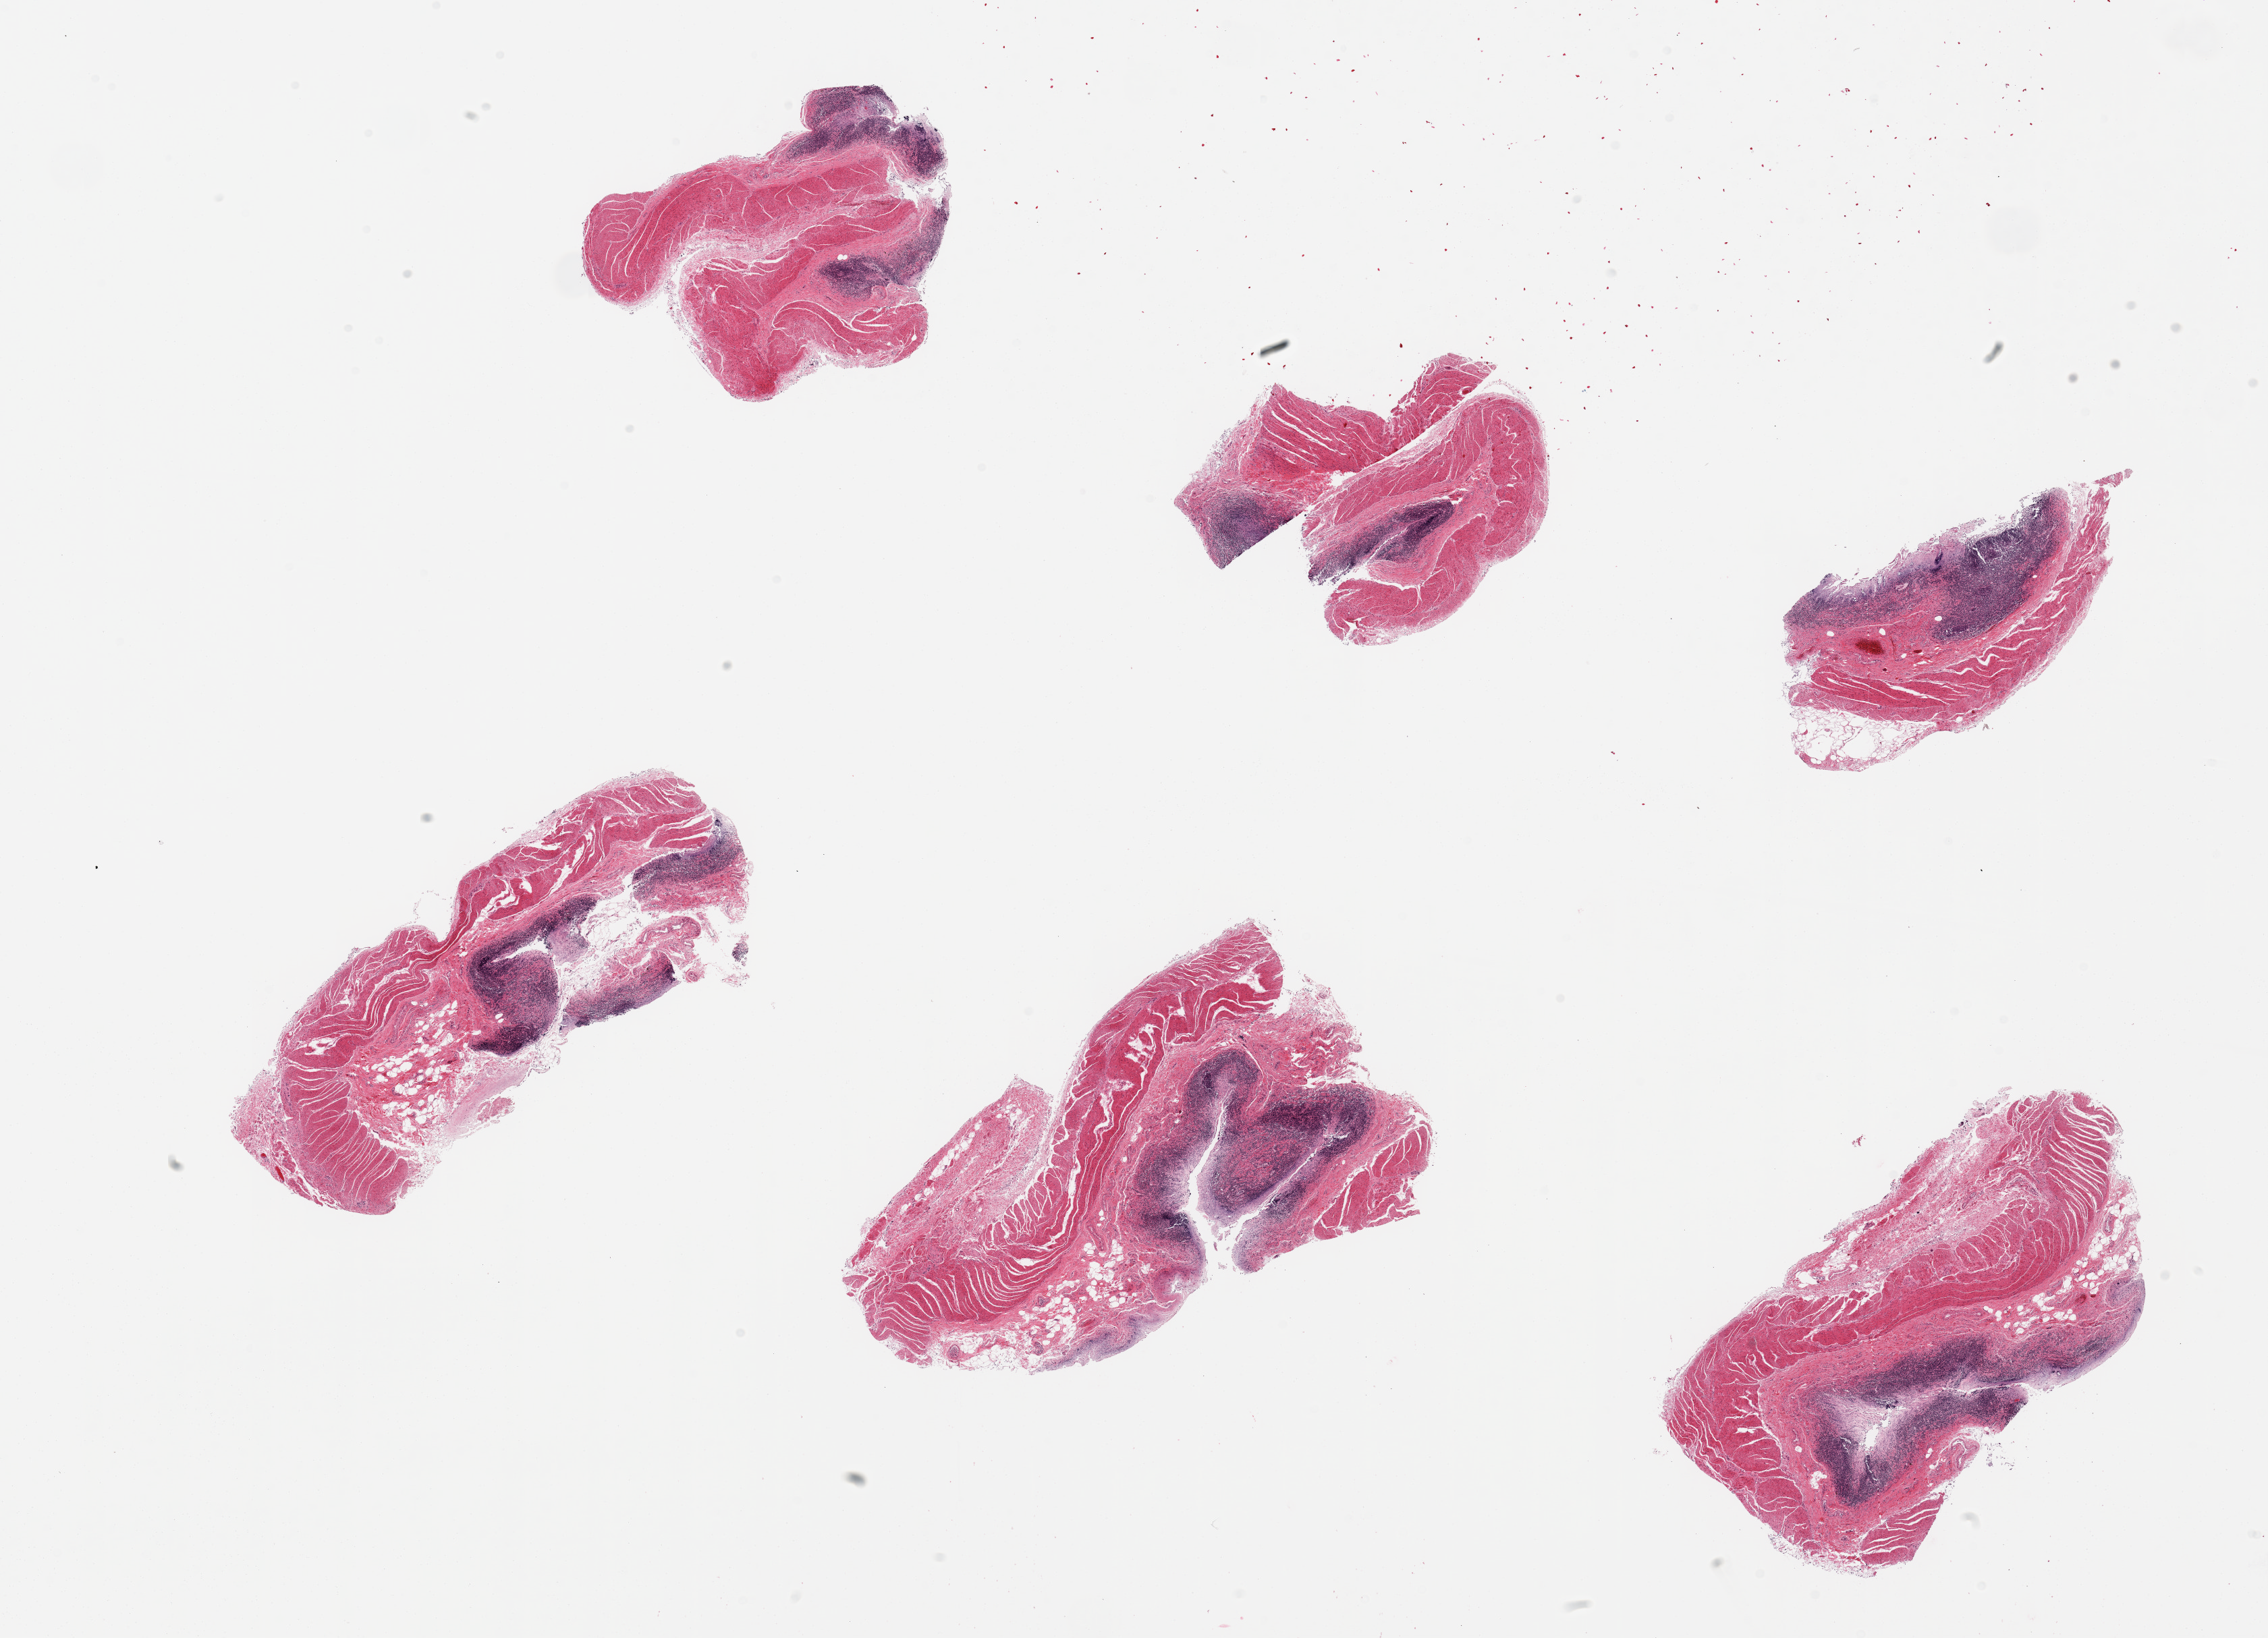
Hematoxylin and eosin (H&E) whole-slide image — whole scanned area (about 26.6 x 19.2 mm) shown as a low-resolution overview; PAXgene-fixed paraffin-embedded (PFPE) section; target tissue: ileum; donor tissue sample. Donor: male.
Reviewer comment on this tissue sample: 6 pieces; lymphoid tissue in each piece, but muscularis propria also present.